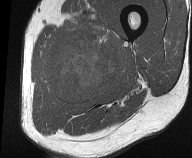
MRI of an extremity soft-tissue mass, one axial slice; slice 18 of 61 in the series (ordered by position); MR volume resampled by the dataset authors to the PET/CT grid (not the native acquisition matrix); 3.27 mm slice thickness; 192 × 158 image matrix, field of view 187 × 154 mm. Male patient. From the clinical record (not read from this slice): histological type: pleiomorphic liposarcoma; grade: high; site of the primary tumour: left thigh.
Outlined on this slice (expert contour drawn on MRI and transferred to this co-registered scan by the dataset authors):
- gross tumour volume including surrounding oedema: box from (x=41, y=19) to (x=126, y=108) px
- gross tumour volume (mass): (x=48, y=41)–(x=110, y=102)